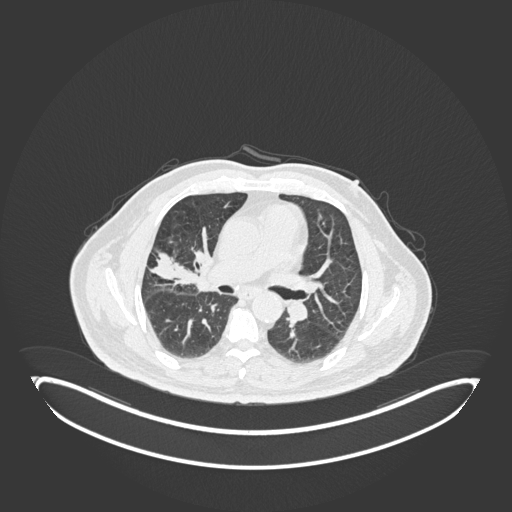
Chest CT, one axial slice; slice 93 of 247 in the series (ordered by position); lung window (W 1500 / L -600 HU); 1 mm slice thickness; 512 × 512 image matrix. Patient: male, 72 years. Case-level facts recorded for this patient, not image findings: clinical TNM (as recorded): T1c N0 M0.
Structures marked on this image (bounding box drawn by a radiologist):
- lung tumour (recorded histology: squamous cell carcinoma): box from (x=183, y=242) to (x=210, y=296) px